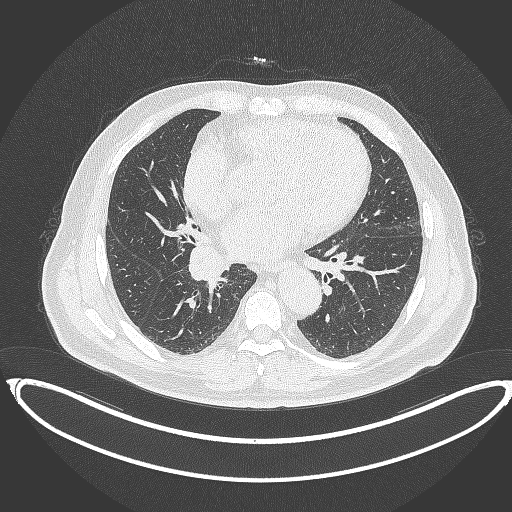
Chest CT, one axial slice. Position 187 of 387 along the scan axis. Reconstruction kernel B70f. 120 kVp. Lung window (W 1500 / L -600 HU). 1 mm slice thickness. 512 × 512 image matrix, field of view 448 × 448 mm. Patient: male, 61 years. From the clinical record (not read from this slice): clinical TNM (as recorded): T1b N1 M0.
Outlined on this slice (bounding box drawn by a radiologist):
- lung tumour (recorded histology: squamous cell carcinoma): bounding box (x1, y1, x2, y2) in pixels: (186, 244, 227, 286)